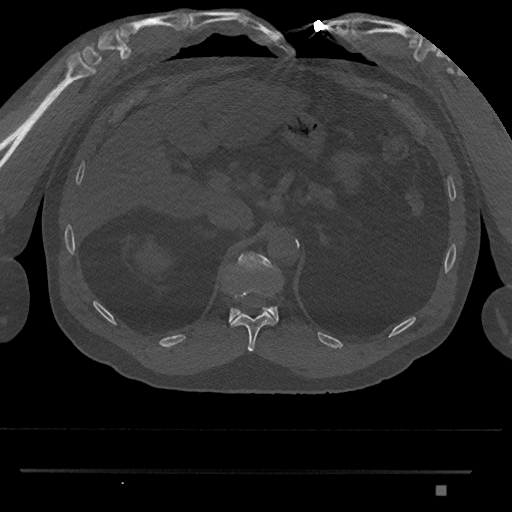
CT including the spine, one axial slice. Slice 925 of 1134 in the series (ordered by position). 120 kVp. Bone window (W 1800 / L 400 HU). 512 × 512 image matrix, field of view 429 × 429 mm. Patient: male, 65 years. Case-level facts recorded for this patient, not image findings: primary cancer: prostate.
Structures marked on this image (semi-automatically segmented with operator editing):
- T11 vertebra: bounding box <230,291,278,352> (left, top, right, bottom; pixels)
- T12 vertebra: <229,252,279,323>